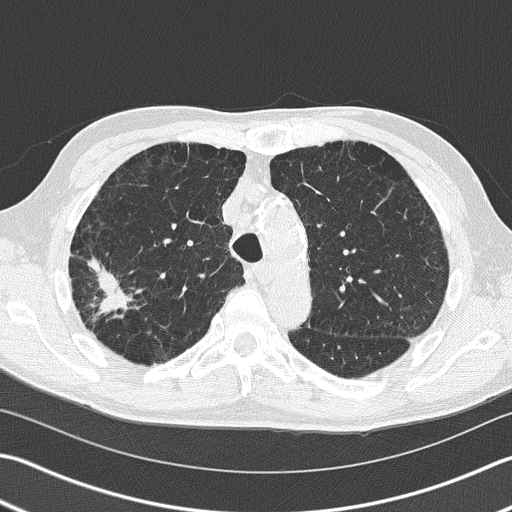
Low-dose screening chest CT, one axial slice. Slice 113 of 163 in the series (ordered by position). Reconstruction kernel B50f. Lung window (W 1500 / L -600 HU). 2 mm slice thickness. 512 × 512 image matrix, field of view 346 × 346 mm.
Annotated regions visible in this slice (expert manual segmentation):
- lesion 1 (tumor, upper lobe of right lung): bounding box [x1, y1, x2, y2] px = [89, 258, 132, 313]